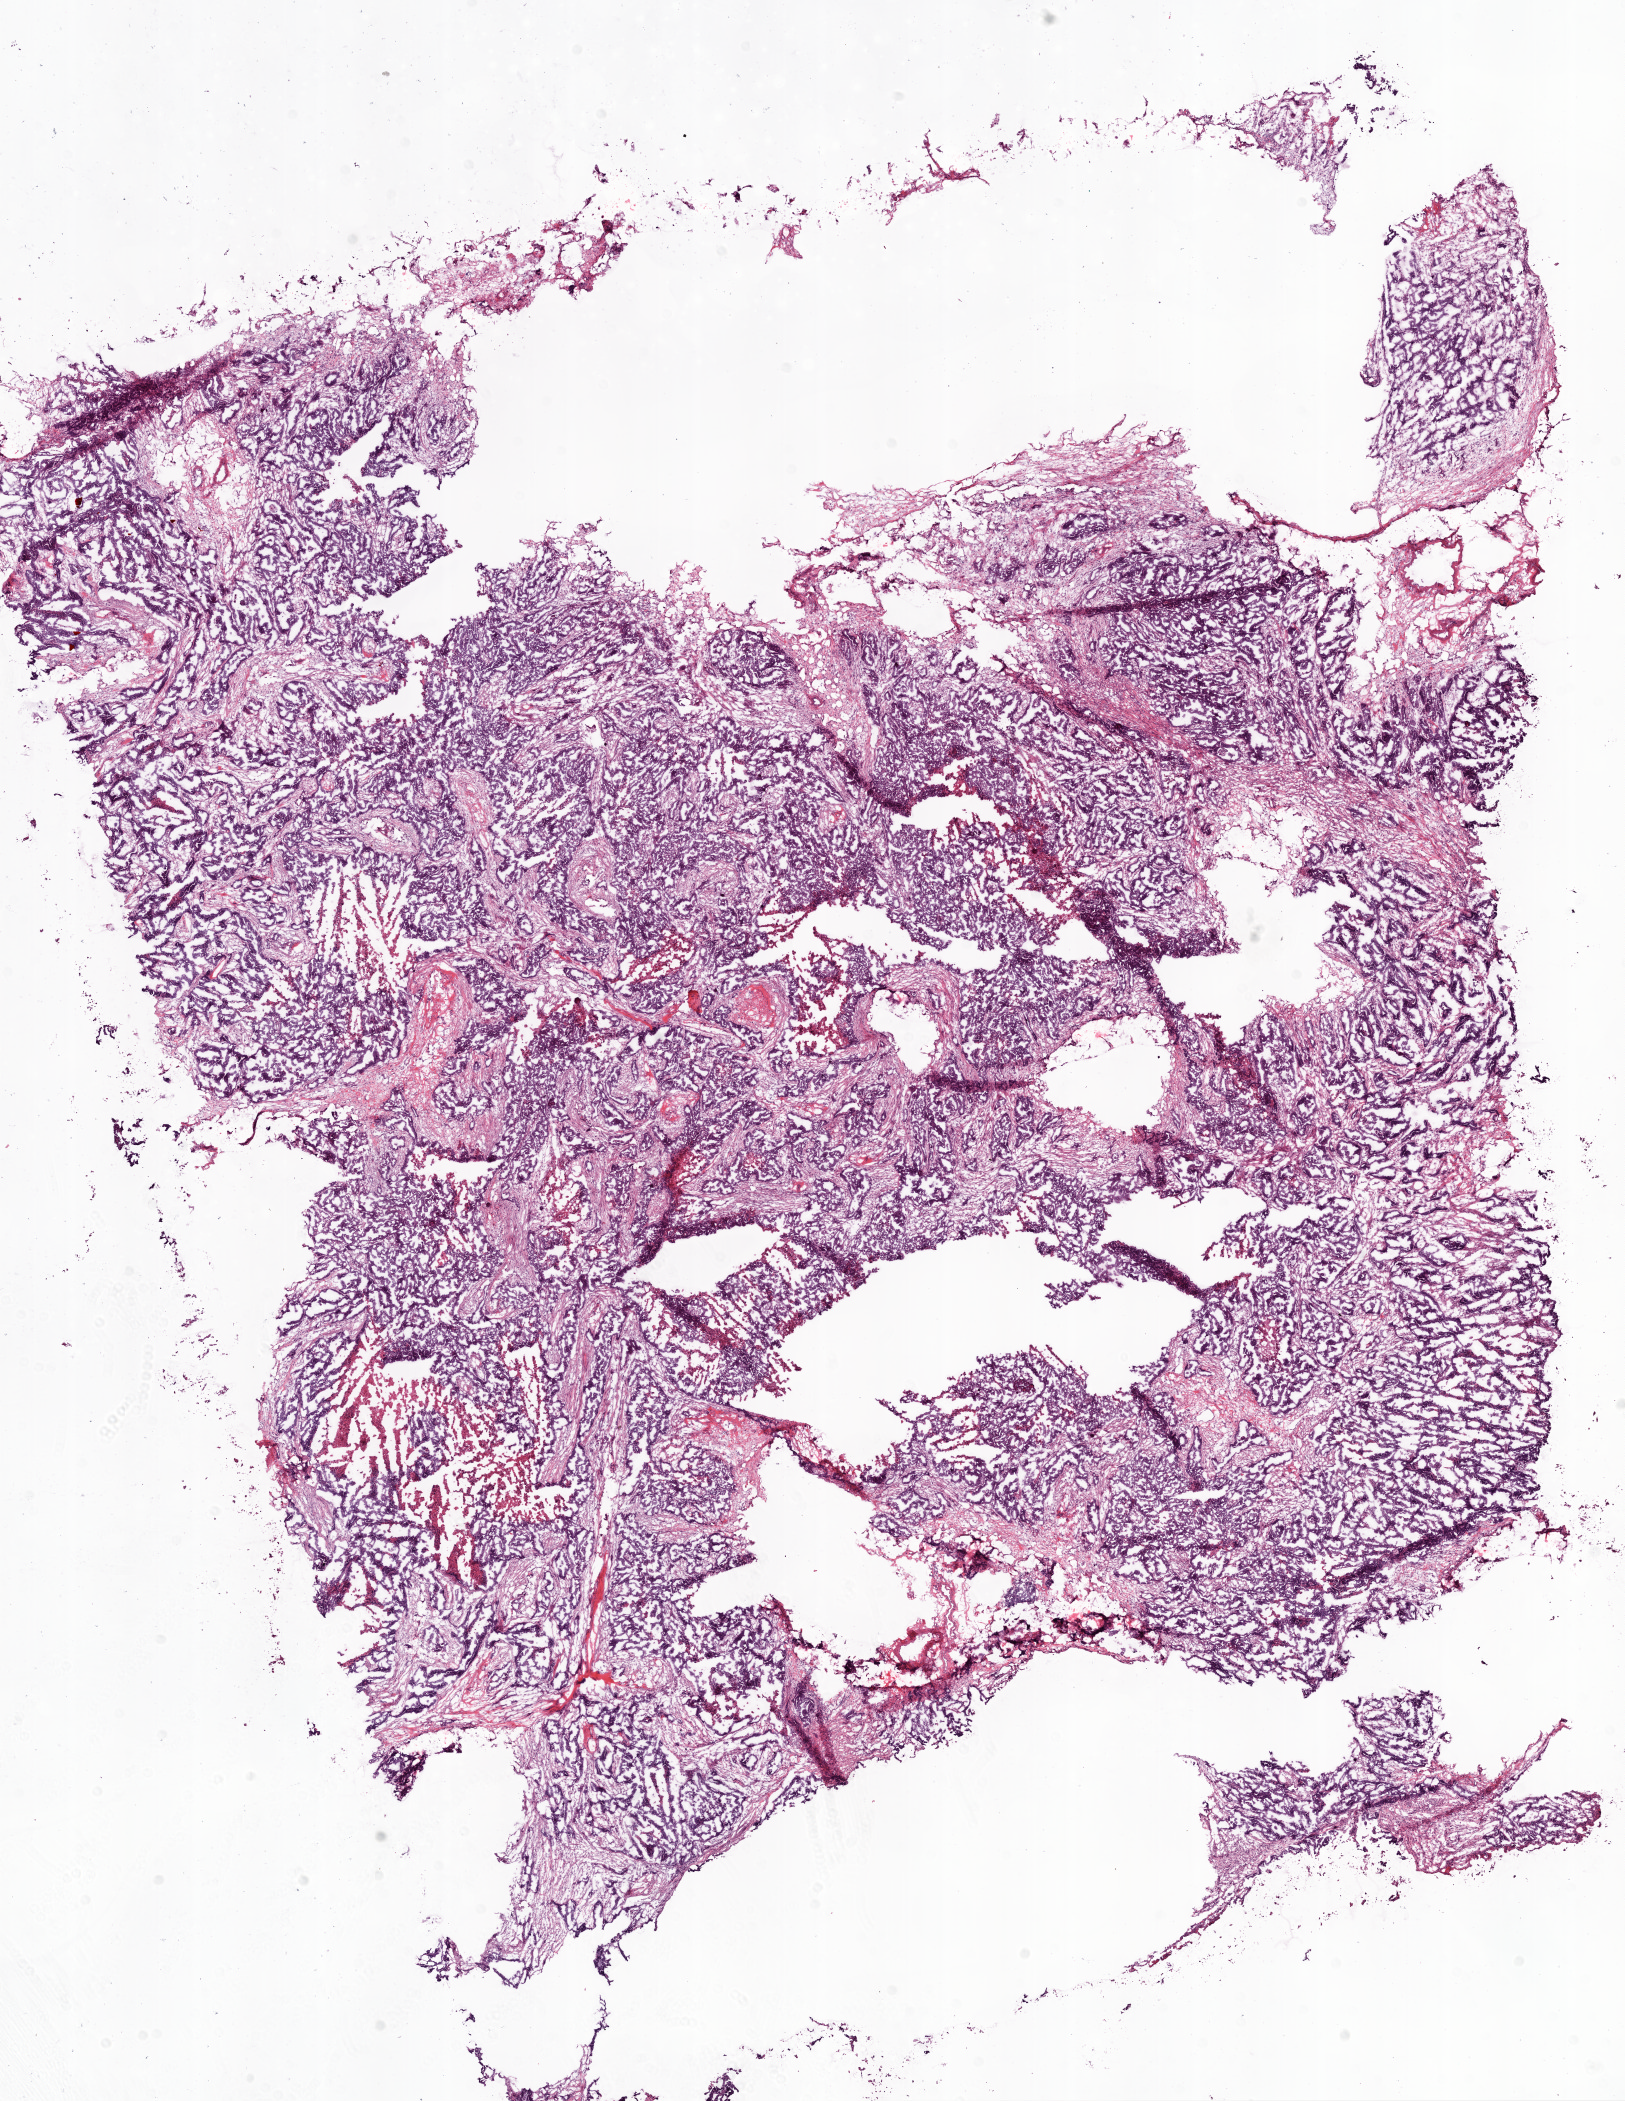
Digitized H&E tissue section (whole slide), shown as a low-resolution overview of the whole scanned area (about 13.0 x 16.9 mm). Frozen section from the bottom of the tissue portion. Primary tumour sample from the ovary. Female, age 74 years at initial diagnosis. Histologic grade: GX (grade cannot be assessed). Pathologist review of this section (percent, as recorded): tumour cells 70%, tumour nuclei 80%, normal cells 0%, stromal cells 30%, necrosis 0%.
FIGO stage: IV. Pathologic diagnosis: Serous cystadenocarcinoma, NOS.